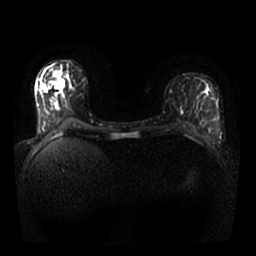
Breast MRI, one axial slice; position 12 of 25 along the scan axis; diffusion-weighted series; image 2 of 4 stored at this slice position (different b-values; order by instance number); 1.5 T; 4 mm slice thickness; 256 × 256 image matrix. Female patient.
Annotated regions visible in this slice (outlined manually by an expert reader):
- tumour on diffusion-weighted imaging: box from (x=53, y=77) to (x=65, y=89) px